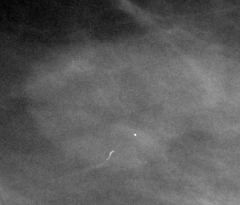
Crop from a digitized film mammogram around one marked abnormality, right breast, MLO view.
Mass, shape lobulated, margins circumscribed; BI-RADS assessment category 3; subtlety rating 5 on a 1 (subtle) to 5 (obvious) scale; benign; no additional work-up was recommended (benign without callback).